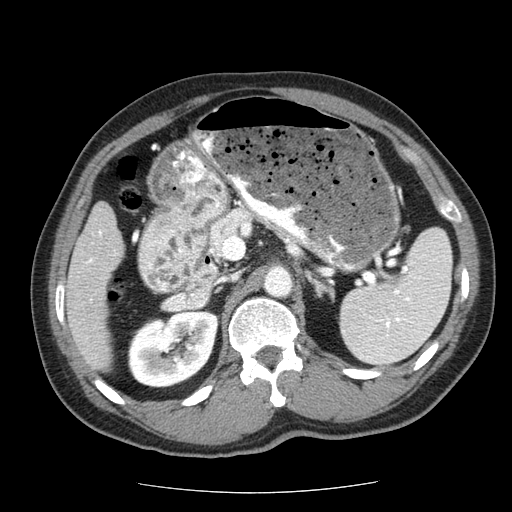
Contrast-enhanced abdominal CT (liver protocol), one axial slice; slice 22 of 85 in the series (ordered by position); 120 kVp; soft-tissue window (W 400 / L 40 HU); 512 × 512 image matrix, field of view 360 × 360 mm. From the clinical record (not read from this slice): diagnosis: hepatocellular carcinoma (patient treated with transarterial chemoembolisation; whether this scan precedes or follows treatment is not stated here); TNM stage (as recorded): Stage-IIIA; Child-Pugh class: A; tumour size: 8 cm.
Structures marked on this image (semi-automatically segmented with operator editing):
- liver parenchyma outside the tumour (the mass and vessels are separate outlines, so this box may not span the whole liver): bounding box <66,202,124,370> (left, top, right, bottom; pixels)
- liver vessels: <85,230,102,264>